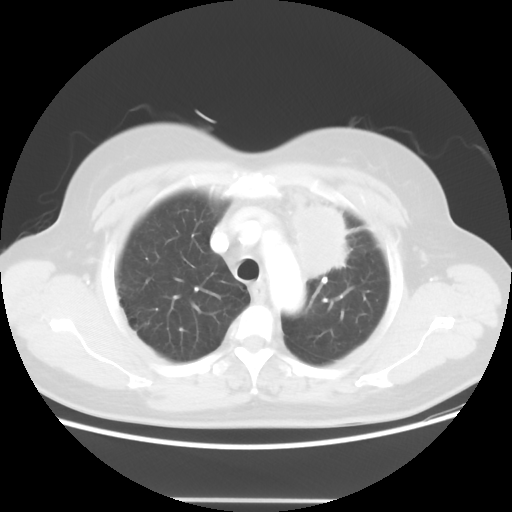
Chest CT, one axial slice. Slice 43 of 52 in the series (ordered by position). 120 kVp. Lung window (W 1500 / L -600 HU). 5 mm slice thickness. 512 × 512 image matrix. Patient: female, 52 years. Case-level facts recorded for this patient, not image findings: clinical TNM (as recorded): T2 N3 M0.
Outlined on this slice (bounding box drawn by a radiologist):
- lung tumour (recorded histology: adenocarcinoma): bounding box [x1, y1, x2, y2] px = [284, 193, 352, 282]